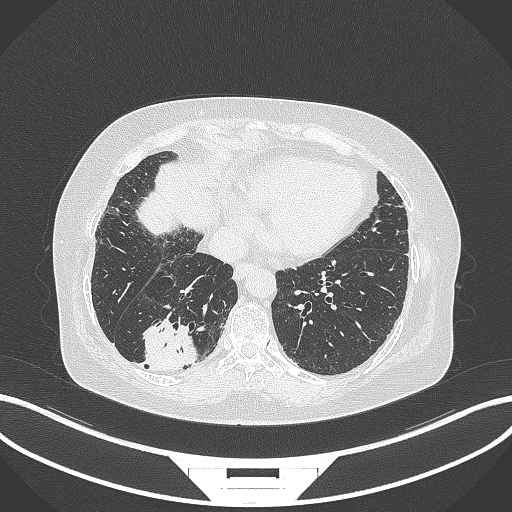
Chest CT, one axial slice. Slice 63 of 296 in the series (ordered by position). 120 kVp. Lung window (W 1500 / L -600 HU). 1 mm slice thickness. 512 × 512 image matrix. Female patient, age 65 years. From the clinical record (not read from this slice): clinical TNM (as recorded): T2b N1 M0; histopathological grade: G1.
Structures marked on this image (bounding box drawn by a radiologist):
- lung tumour (recorded histology: adenocarcinoma): bounding box <140,313,201,373> (left, top, right, bottom; pixels)